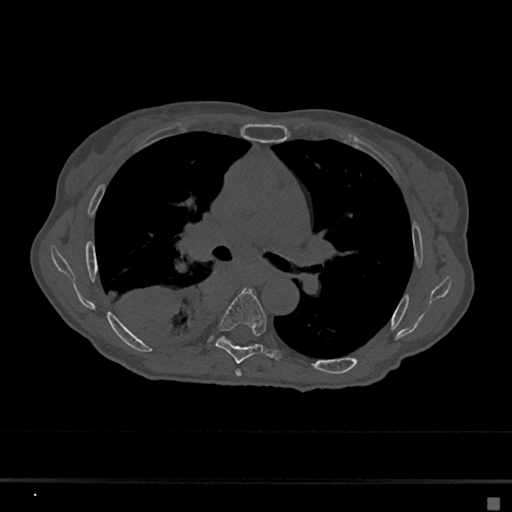
CT including the spine, one axial slice. Position 416 of 797 along the scan axis. Reconstruction kernel Br40s/3. Bone window (W 1800 / L 400 HU). 0.5 mm slice thickness. 512 × 512 image matrix, field of view 360 × 360 mm. Female patient, age 68 years. Case-level facts recorded for this patient, not image findings: primary cancer: renal.
Outlined on this slice (semi-automatic segmentation, software-assisted and operator-edited):
- T5 vertebra: bounding box (x1, y1, x2, y2) in pixels: (235, 369, 242, 377)
- T6 vertebra: (215, 288, 282, 364)